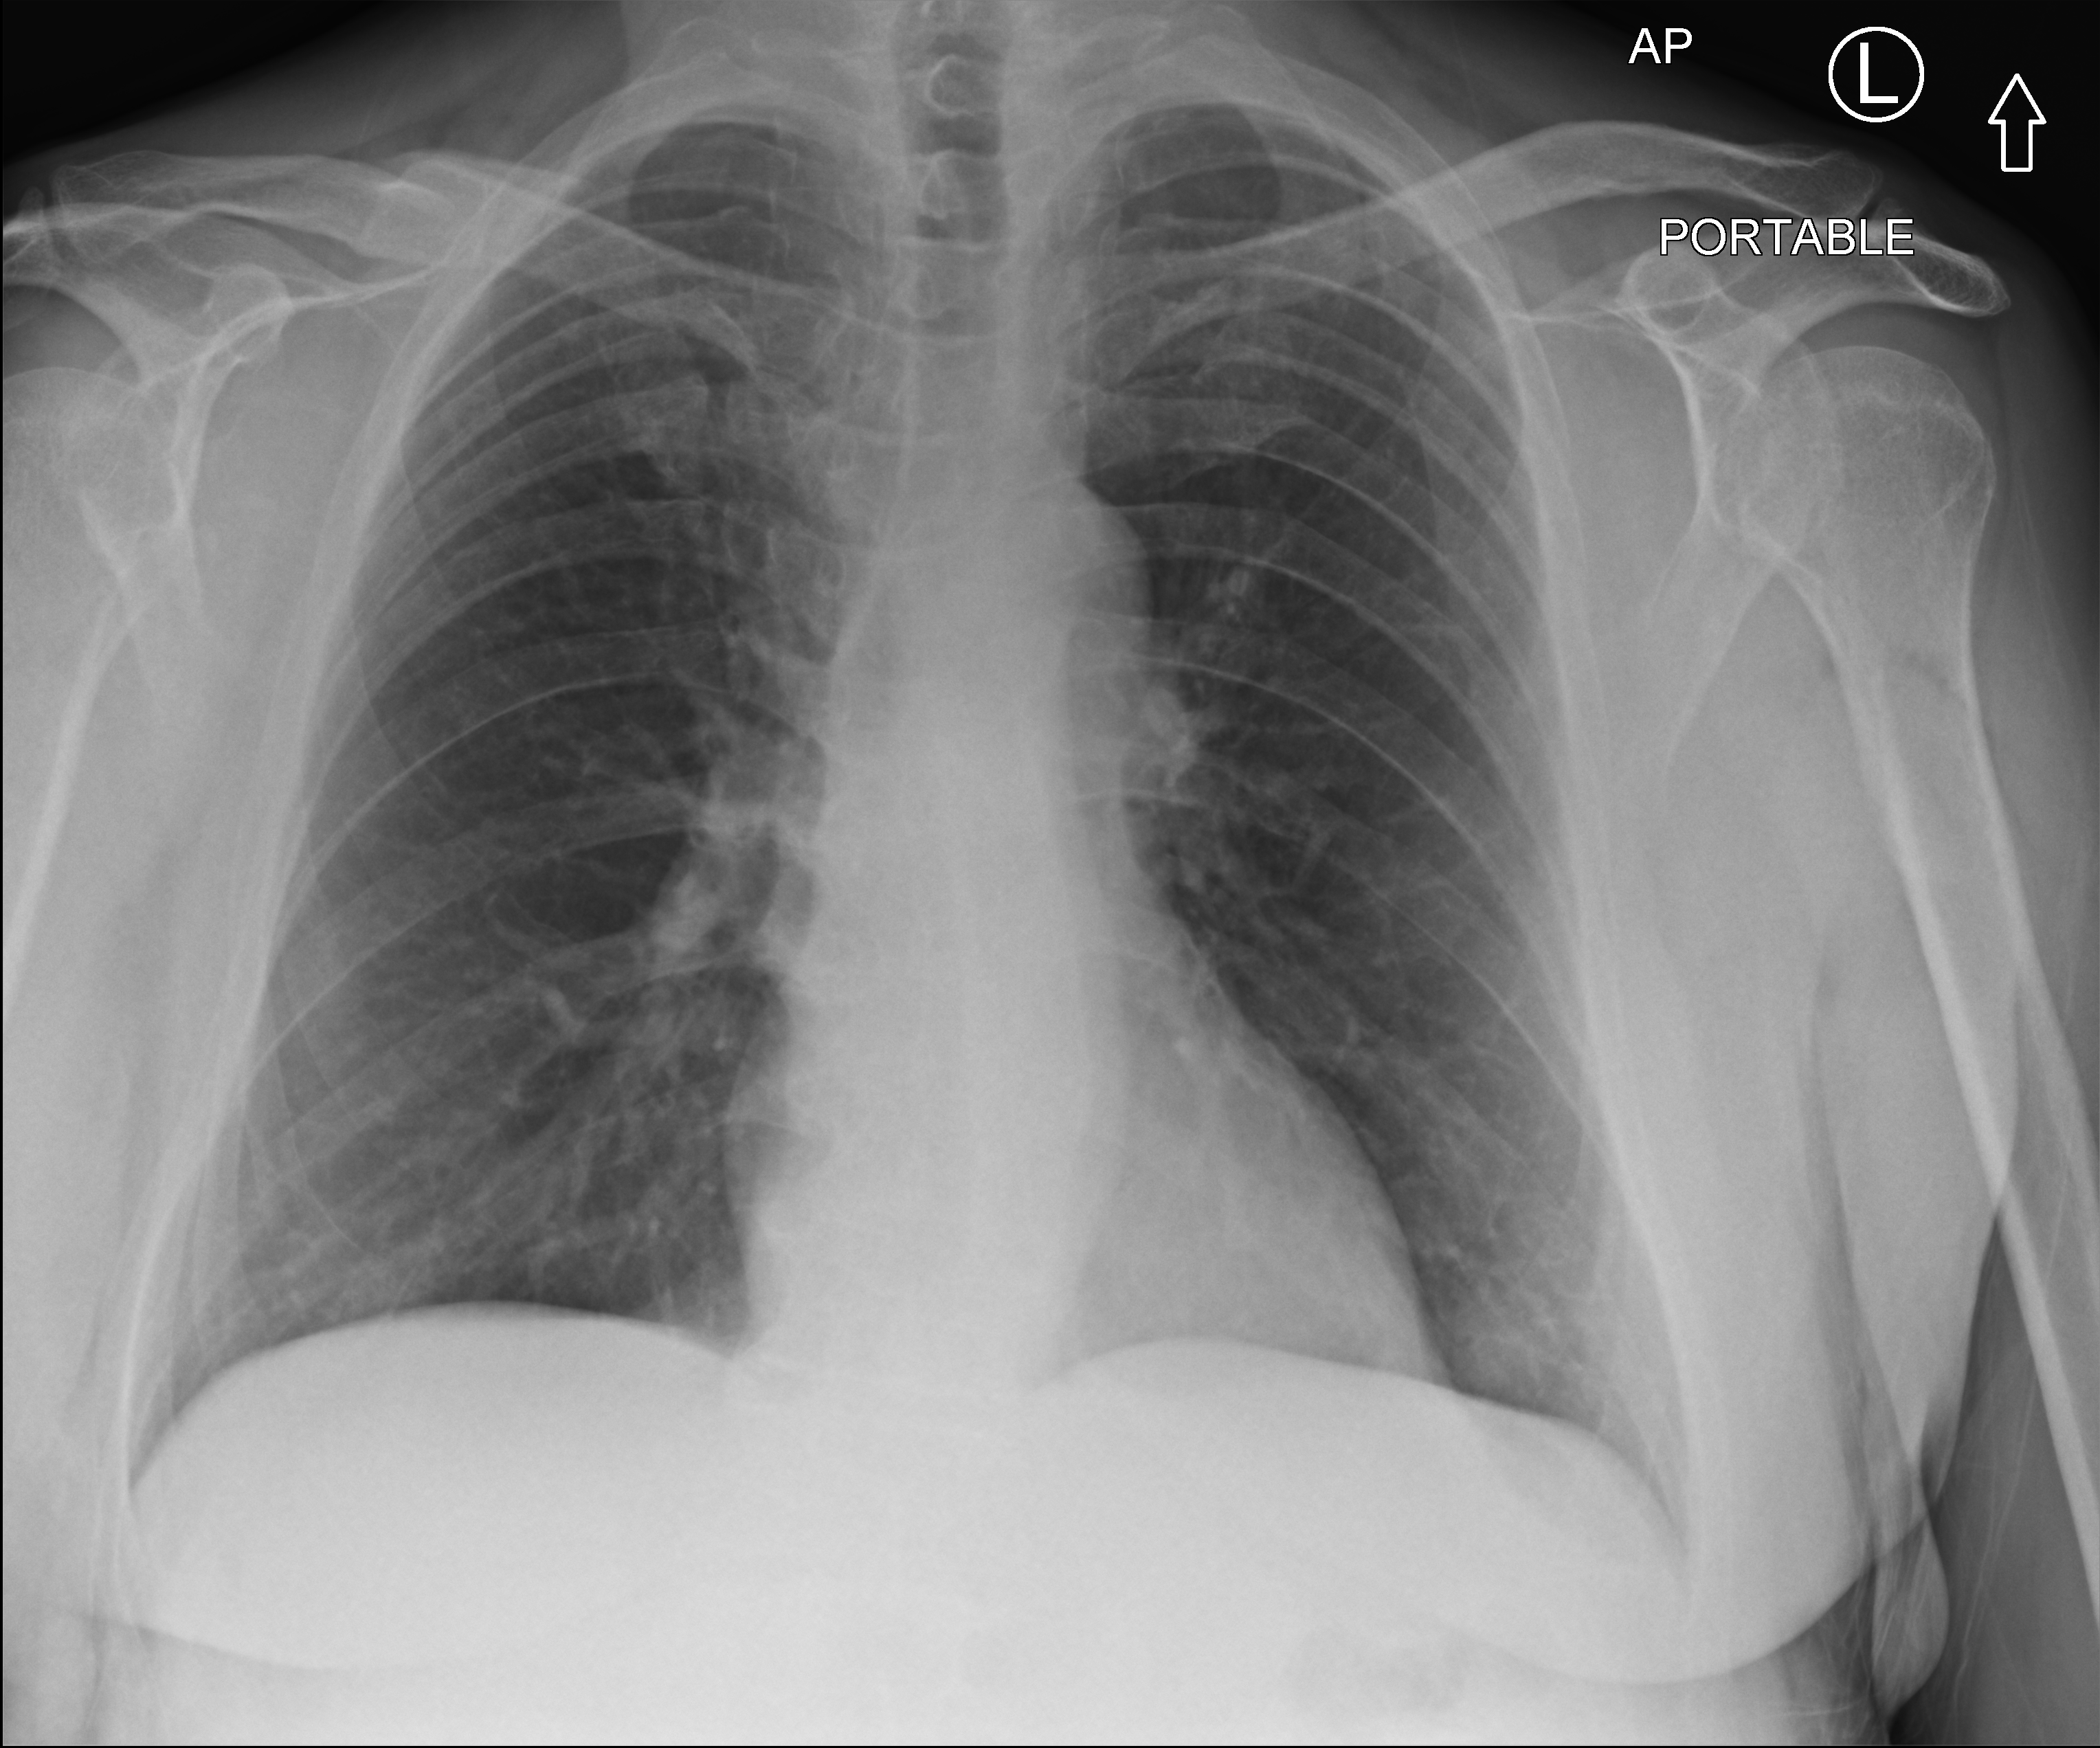
Chest X-ray (portable). Patient hospitalised with COVID-19; male, aged 60–74 years.
Admission-level facts for this patient (not findings on this image; timing relative to this image not recorded): mechanically ventilated during this hospital stay: no.